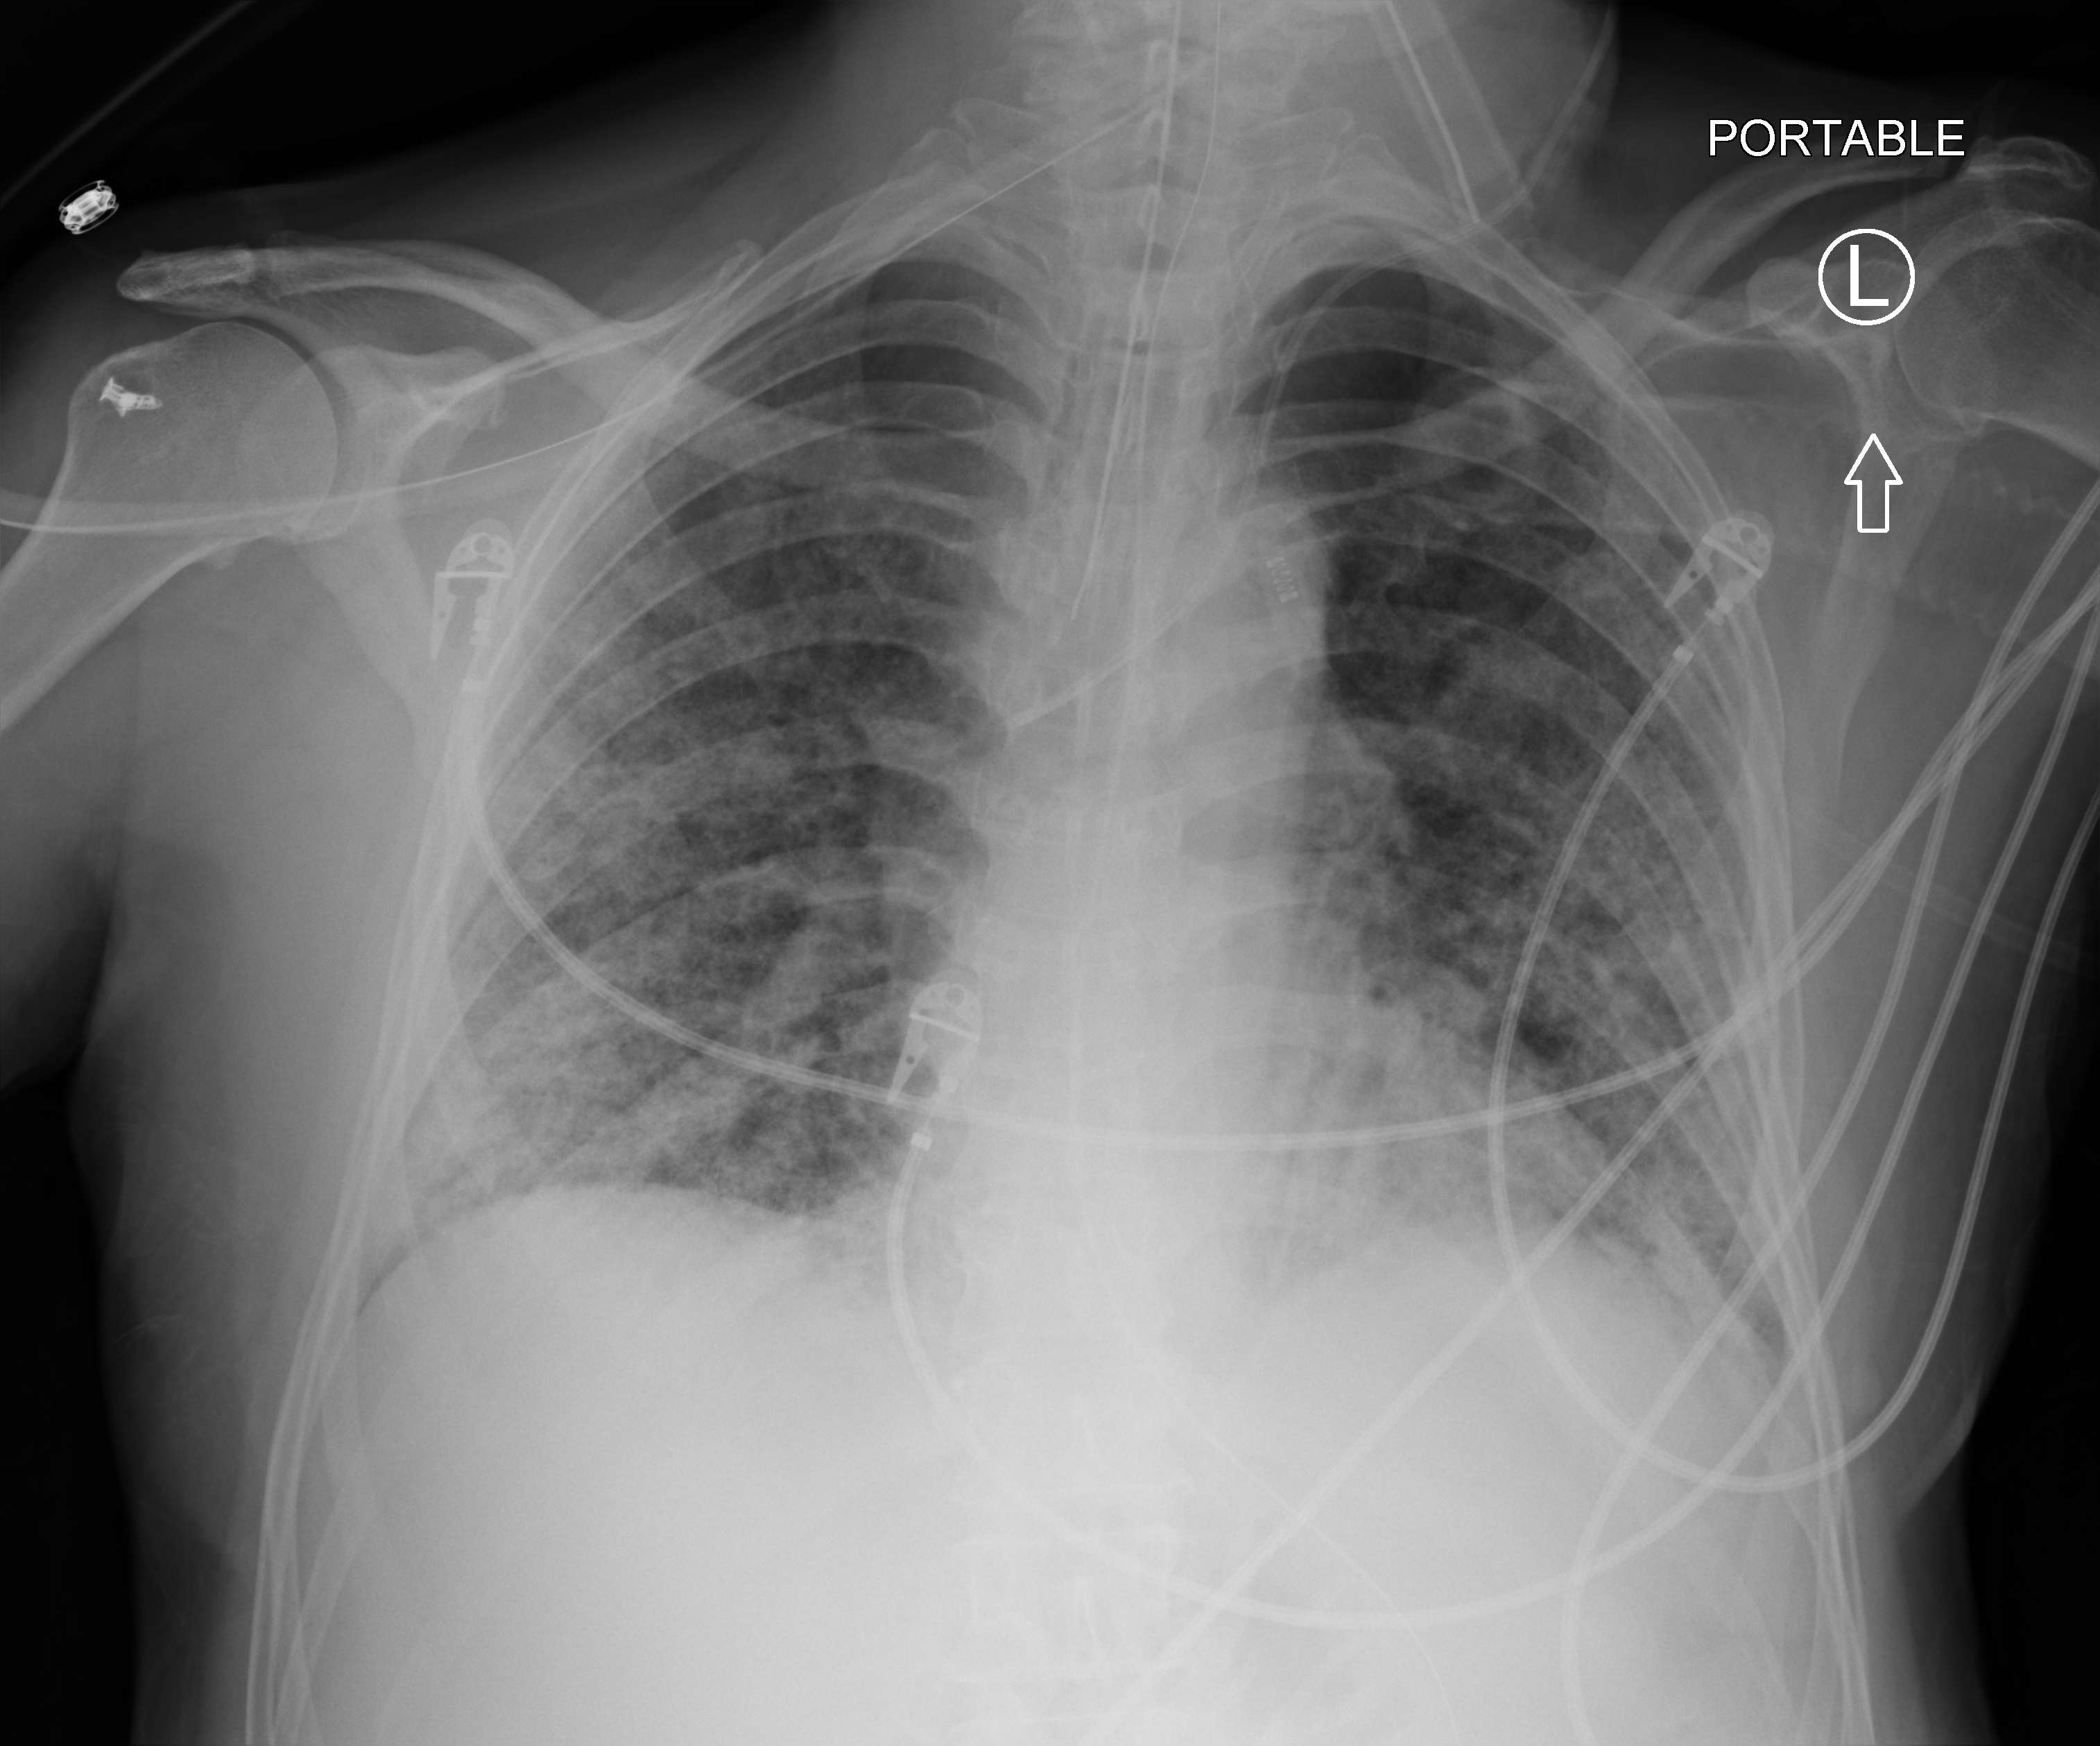
Bedside chest radiograph (computed radiography), anteroposterior (AP) projection. Patient hospitalised with COVID-19; male, aged 60–74 years.
Hospital-stay facts (about this admission, not read from this image; timing relative to this image not recorded):
- admitted to intensive care during this hospital stay: yes